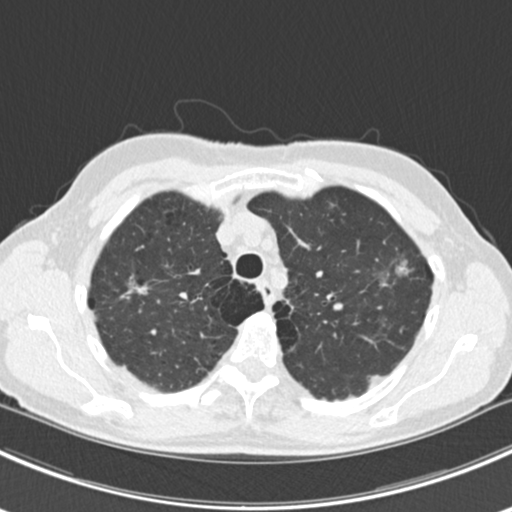
Chest CT (low-dose screening protocol), one axial image. Baseline annual screen. Lung window (W 1500 / L -600 HU). 2 mm slice thickness. Standard (soft-tissue) reconstruction kernel (B30f). Slice 44 of 224 in the series. 512 × 512 image matrix, field of view 310 × 310 mm. Female, age 63 years at enrolment. Current smoker at enrolment.
• Expert reader's lesion annotation, box from (x=364, y=240) to (x=433, y=310) px.
• The screening reader recorded 10 non-calcified nodules or masses ≥4 mm on this exam (right lower lobe, right lower lobe, left lower lobe, left lower lobe, right middle lobe, right lower lobe, left lower lobe, left upper lobe, right upper lobe, left upper lobe); which of them this box marks is not recorded.